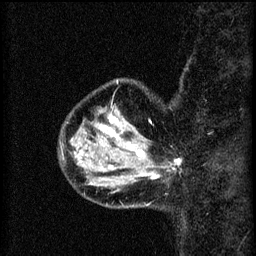
Breast MRI (dynamic contrast-enhanced), one sagittal slice. Position 13 of 60 along the scan axis. 3 images stored at this slice position (order not interpretable as contrast timing). 1.5 T. TE 4.2 ms, TR 8.2 ms. 2 mm slice thickness. 256 × 256 image matrix, field of view 180 × 180 mm. Patient: female, 37 years.
Annotated regions visible in this slice (semi-automatically segmented with operator editing):
- analysis volume of interest (the breast-tissue region the enhancement analysis was run in; not a lesion): bounding box <124,138,182,185> (left, top, right, bottom; pixels)
- tumour enhancement mask (voxels above the 70 % enhancement threshold inside the analysis volume of interest): <128,144,181,179>